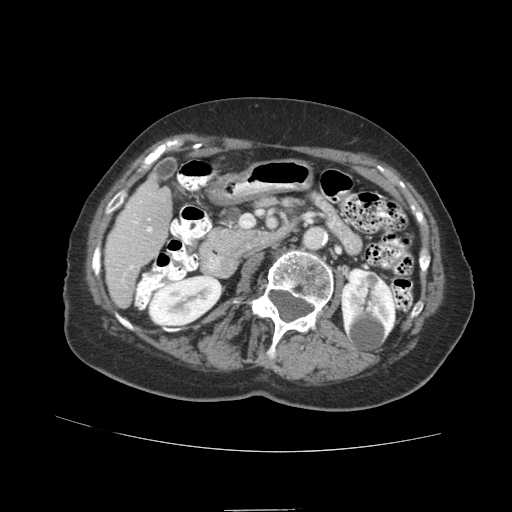
Contrast-enhanced abdominal CT (liver protocol), one axial slice. Soft-tissue window (W 400 / L 40 HU). 2.5 mm slice thickness. 512 × 512 image matrix, field of view 360 × 360 mm. Case-level facts recorded for this patient, not image findings: diagnosis: hepatocellular carcinoma (patient treated with transarterial chemoembolisation; whether this scan precedes or follows treatment is not stated here); TNM stage (as recorded): Stage-II; Child-Pugh class: A; tumour nodularity: multinodular; tumour size: 4 cm.
Structures marked on this image (semi-automatically segmented with operator editing):
- liver parenchyma outside the tumour (the mass and vessels are separate outlines, so this box may not span the whole liver): box from (x=104, y=176) to (x=172, y=308) px
- liver vessels: (x=122, y=201)–(x=152, y=281)